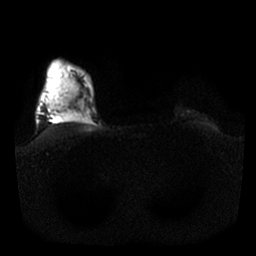
Breast MRI, one axial slice; slice 23 of 25 in the series (ordered by position); diffusion-weighted series; image 2 of 4 stored at this slice position (different b-values; order by instance number); 1.5 T; 4 mm slice thickness; 256 × 256 image matrix, field of view 340 × 340 mm. Female patient.
Structures marked on this image (outlined manually by an expert reader):
- tumour on diffusion-weighted imaging: bounding box <45,59,83,113> (left, top, right, bottom; pixels)